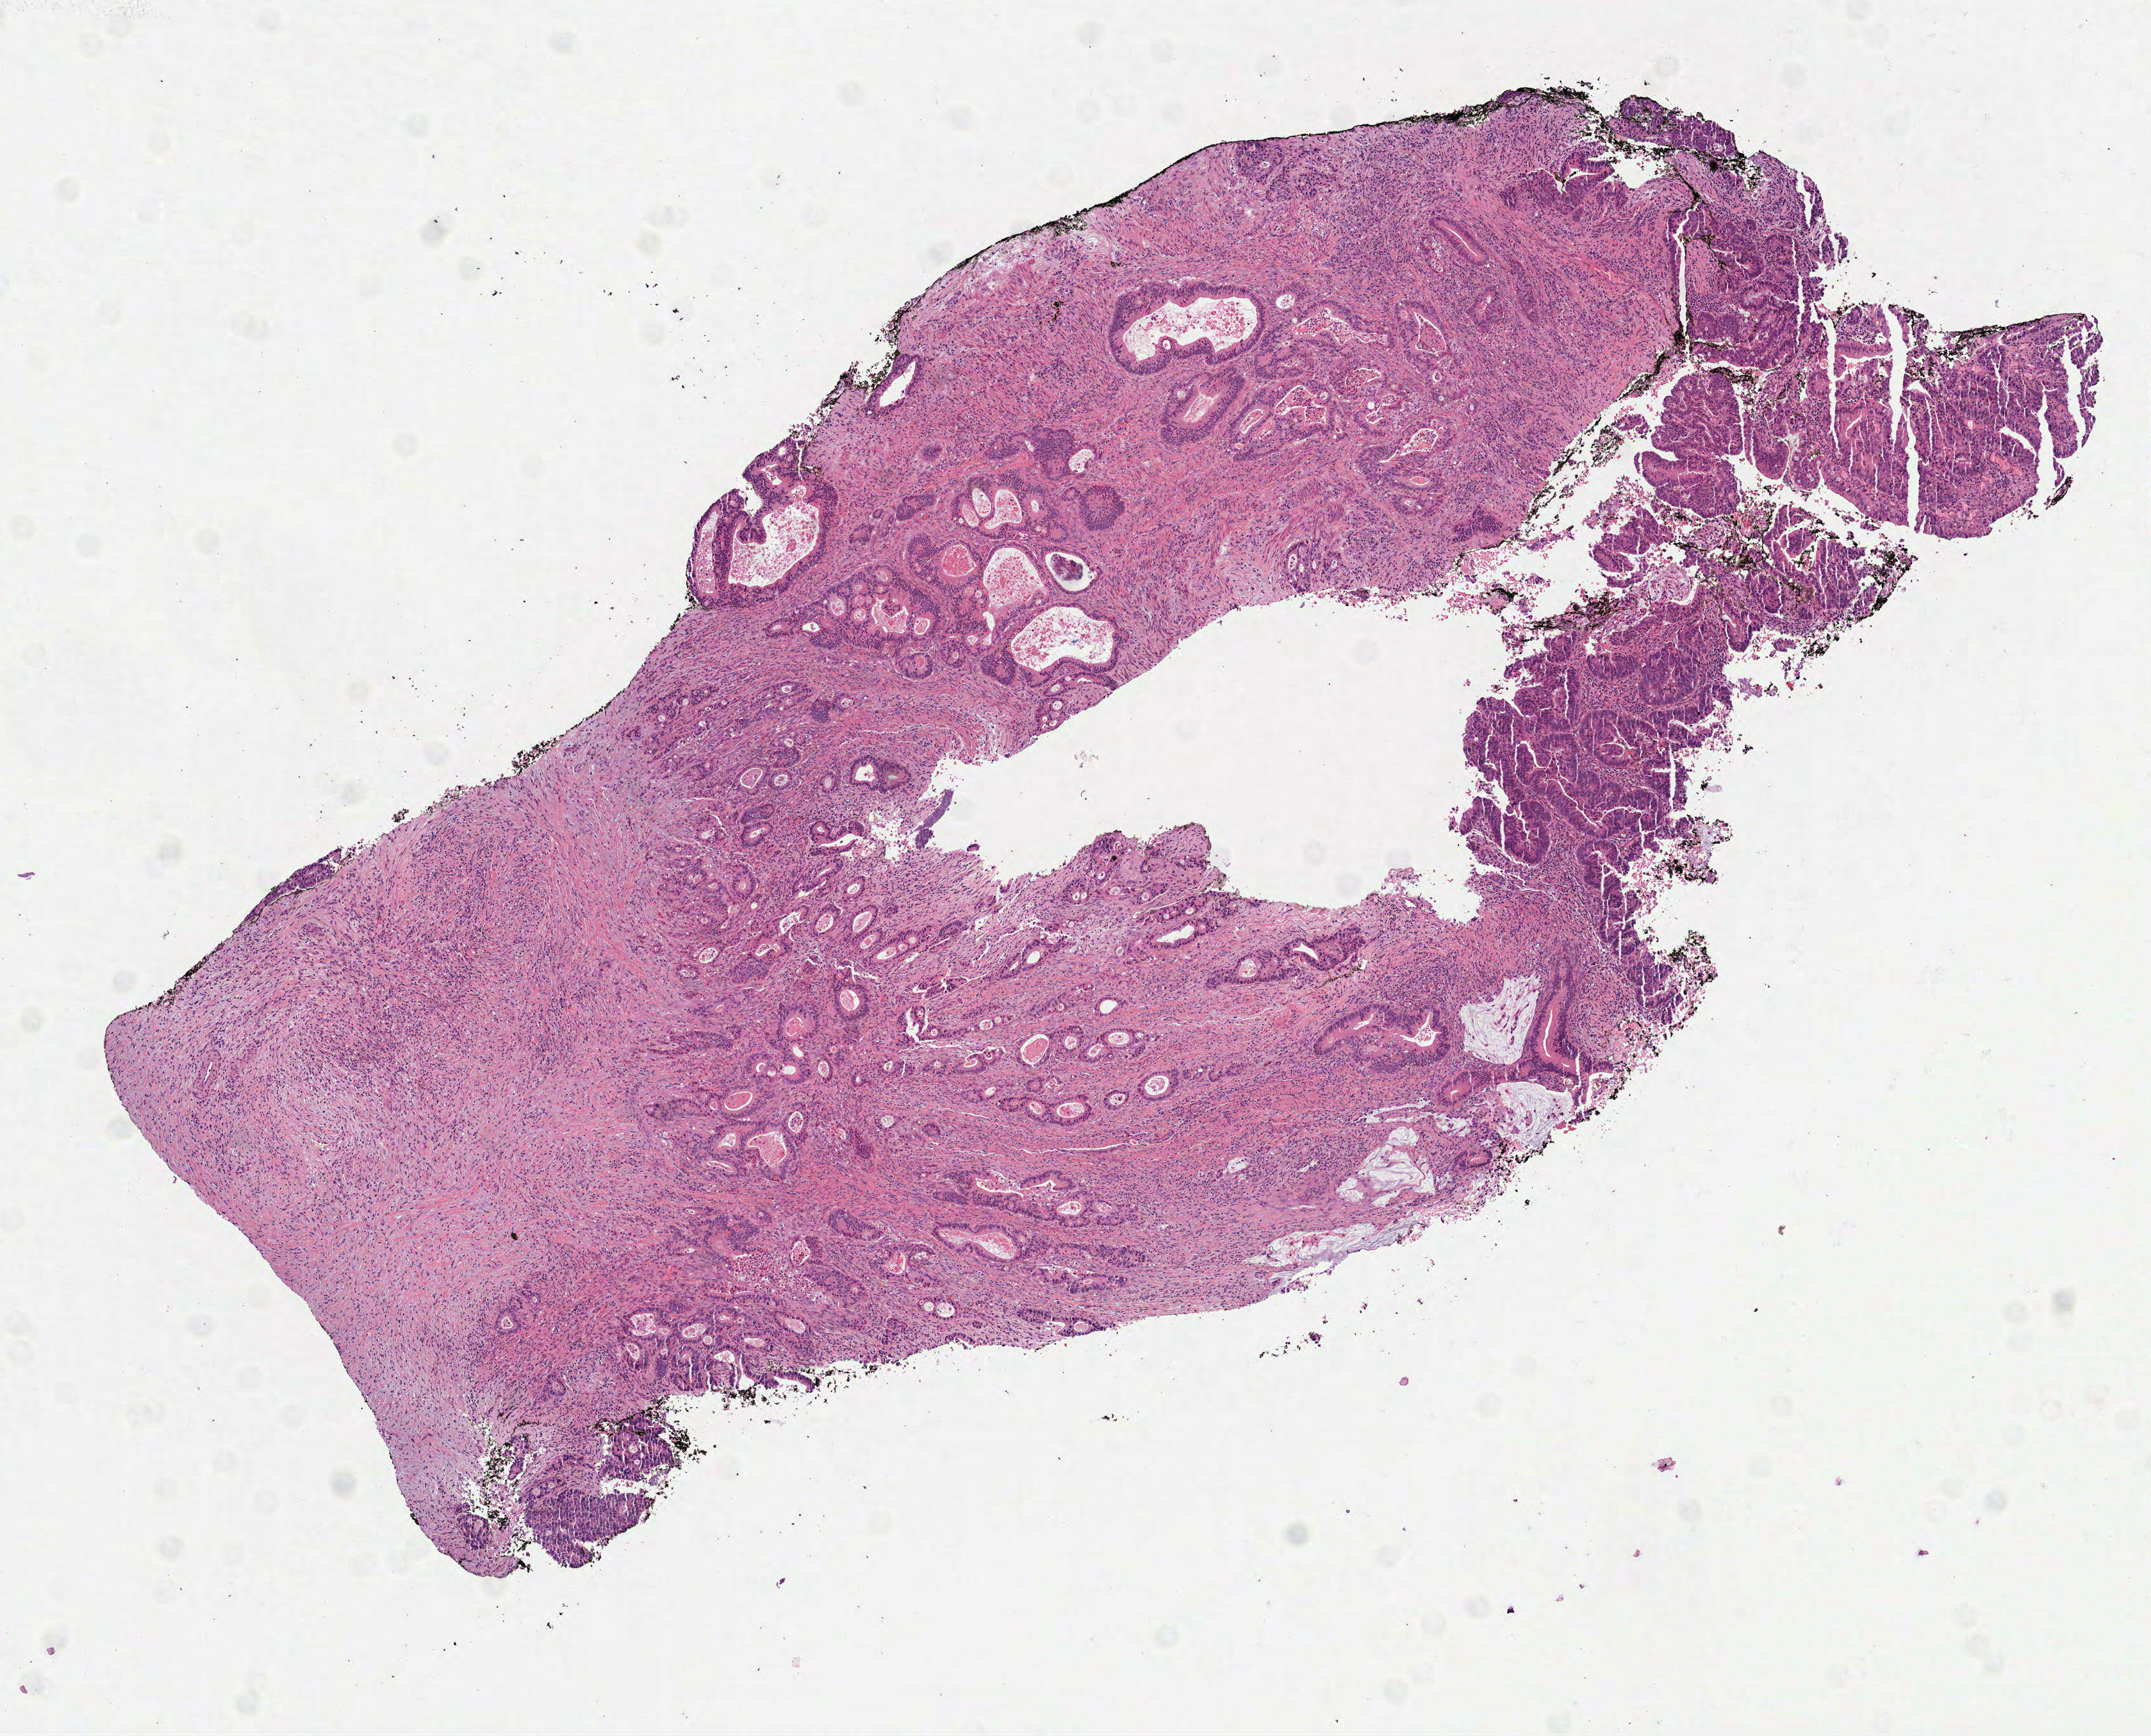
Whole-slide histology image, H&E-stained, a low-resolution overview of the entire scanned area, about 6.8 x 5.5 mm (acquisition: 40x scan). Formalin-fixed paraffin-embedded (FFPE) diagnostic section. Primary tumour sample from the colon. Patient: male, age at initial diagnosis 84 years.
* lymph nodes positive (case pathology): 17 of 20 examined
* AJCC pathologic stage: IIIC (7th edition)
* histologic diagnosis: Mucinous adenocarcinoma